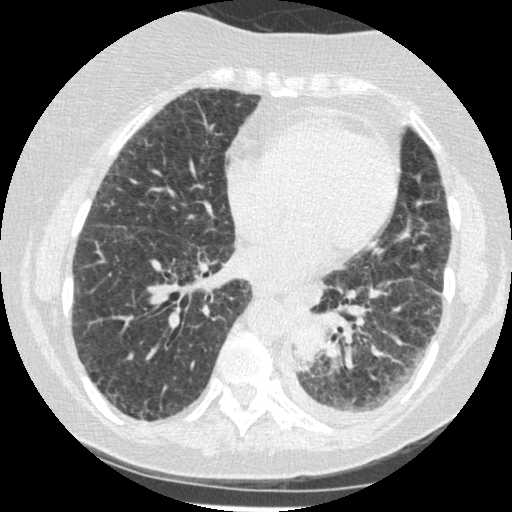
Low-dose screening chest CT, axial slice; third screening round (two years after baseline); lung window (W 1500 / L -600 HU); standard (soft-tissue) reconstruction kernel (STANDARD); 120 kVp. Female, age 60 years at enrolment. Former smoker at enrolment.
- Expert reader's lesion annotation, bounding box [x1, y1, x2, y2] px = [279, 301, 344, 376].
- Screening reader's record for this exam (one nodule recorded; not confirmed to be the boxed lesion): non-calcified nodule or mass ≥4 mm, left lower lobe, 54 × 38 mm, smooth margins, soft tissue attenuation, pre-existing on the prior screen: yes; interval growth: yes.
- Official screen result: positive, other.